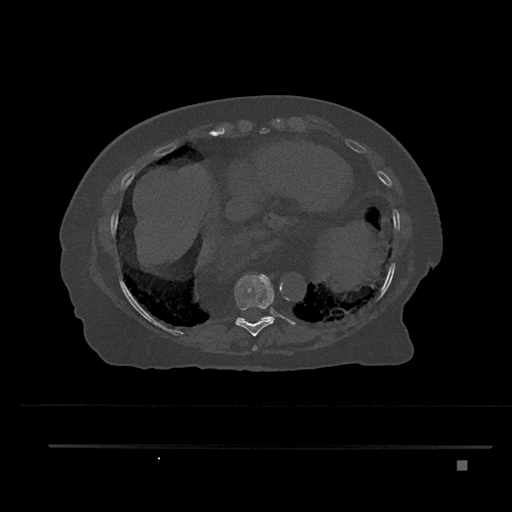
CT including the spine, one axial slice; slice 391 of 797 in the series (ordered by position); 120 kVp; bone window (W 1800 / L 400 HU); 512 × 512 image matrix, field of view 437 × 437 mm. Patient: female, 76 years. Case-level facts recorded for this patient, not image findings: primary cancer: lung; vertebrae with lytic lesions (as recorded): T11, L3.
Annotated regions visible in this slice (semi-automatic segmentation, software-assisted and operator-edited):
- T10 vertebra: box from (x=242, y=316) to (x=271, y=320) px
- T8 vertebra: (x=252, y=346)–(x=257, y=351)
- T9 vertebra: (x=235, y=274)–(x=274, y=337)